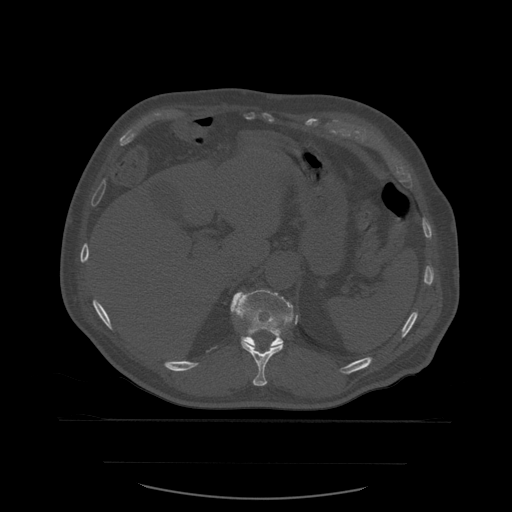
CT including the spine, one axial slice; slice 286 of 590 in the series (ordered by position); bone window (W 1800 / L 400 HU); 1.25 mm slice thickness; 512 × 512 image matrix, field of view 479 × 479 mm. Patient age 71 years. Case-level facts recorded for this patient, not image findings: primary cancer: lung; vertebrae with lytic lesions (as recorded): T1, T2, L5, S1.
Annotated regions visible in this slice (semi-automatically segmented with operator editing):
- T11 vertebra: bounding box <241,316,298,386> (left, top, right, bottom; pixels)
- T12 vertebra: <230,289,299,350>